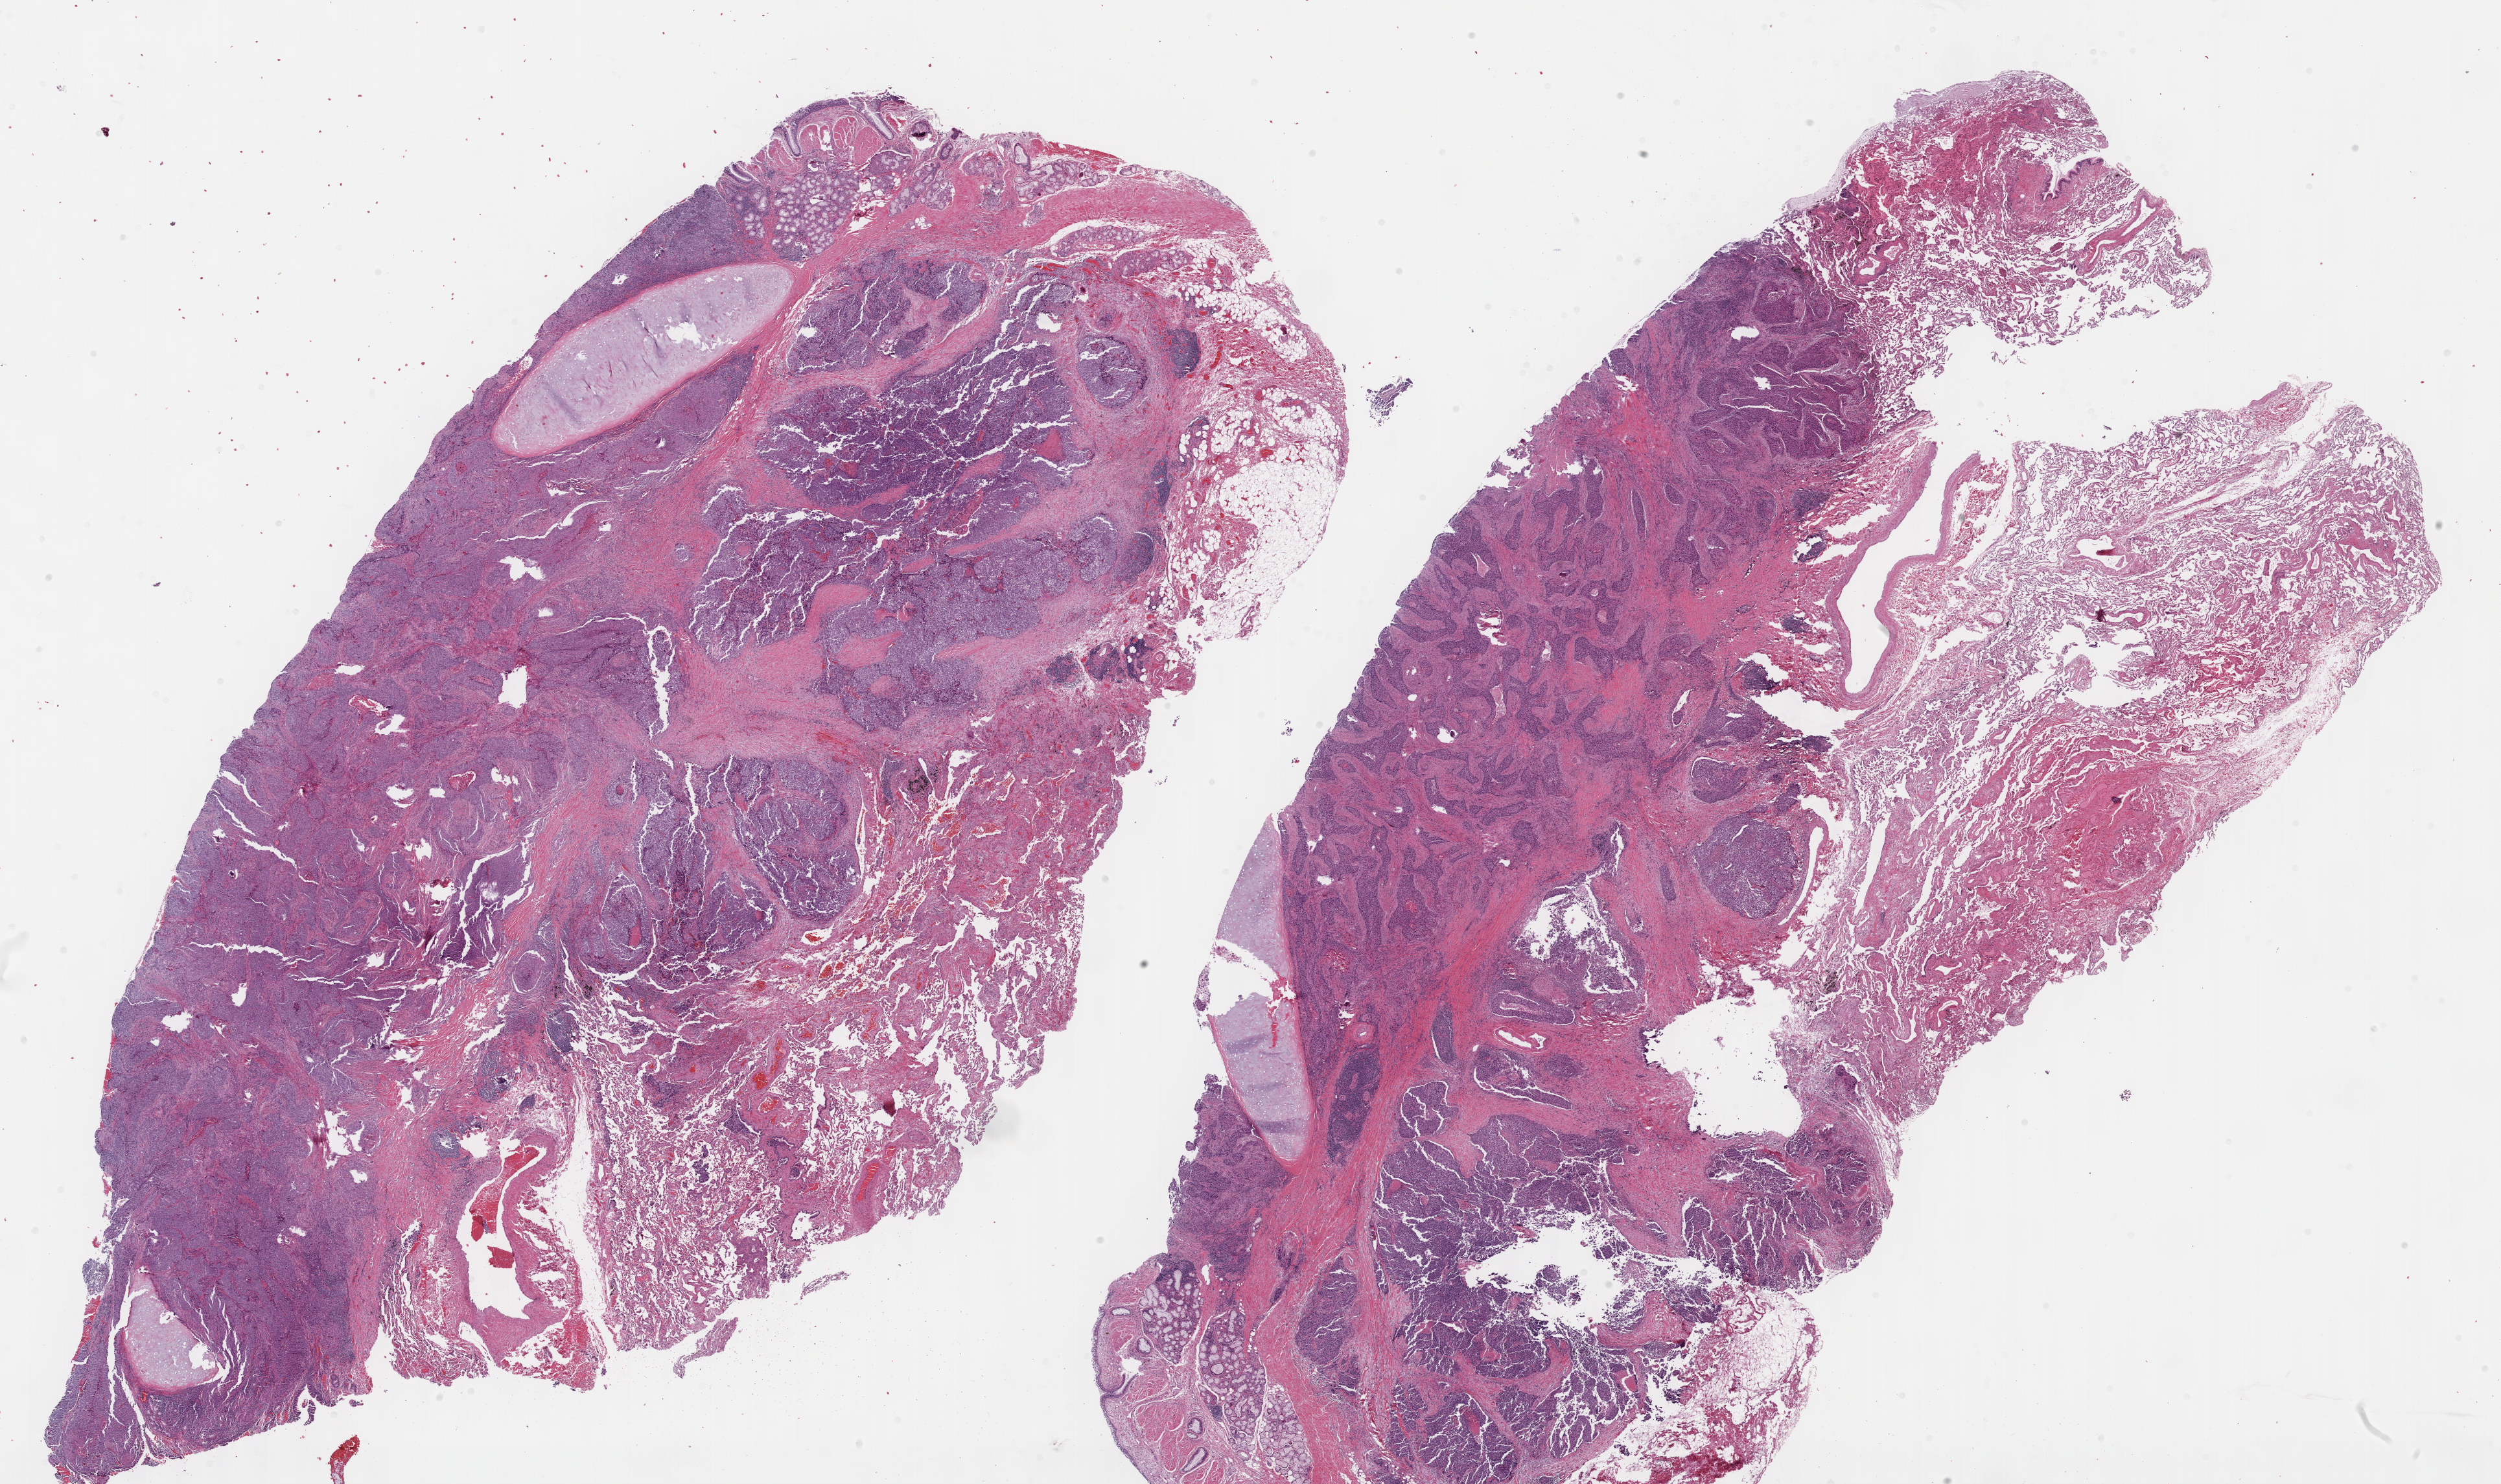
Digitized H&E tissue section (whole slide), shown as a low-resolution overview of the whole scanned area (about 31.2 x 18.5 mm, slide scanned at 40x). Formalin-fixed paraffin-embedded (FFPE) diagnostic section. Sample: primary tumour, lung. Male, age 75 years at initial diagnosis.
- histologic diagnosis: Squamous cell carcinoma, NOS (lower lobe, lung)
- TNM: T2 N0 M0
- laterality: left
- AJCC pathologic stage: IB (6th edition)